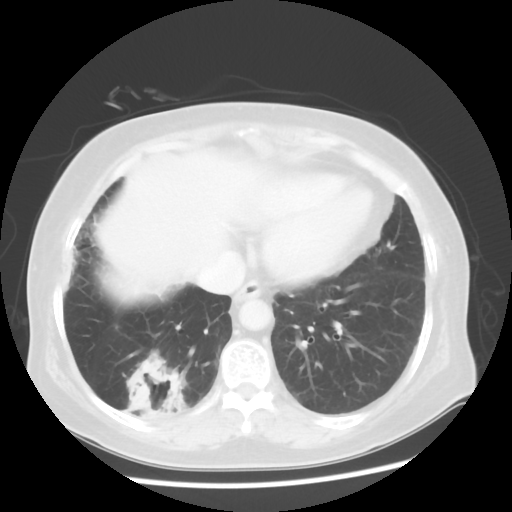
Chest CT, one axial slice; position 17 of 56 along the scan axis; lung window (W 1500 / L -600 HU); 5 mm slice thickness; 512 × 512 image matrix. Patient: female, 64 years. Case-level facts recorded for this patient, not image findings: clinical TNM (as recorded): Tis N0 M0.
Structures marked on this image (rectangle marked by the reading radiologist):
- lung tumour (recorded histology: adenocarcinoma): box from (x=113, y=350) to (x=195, y=431) px